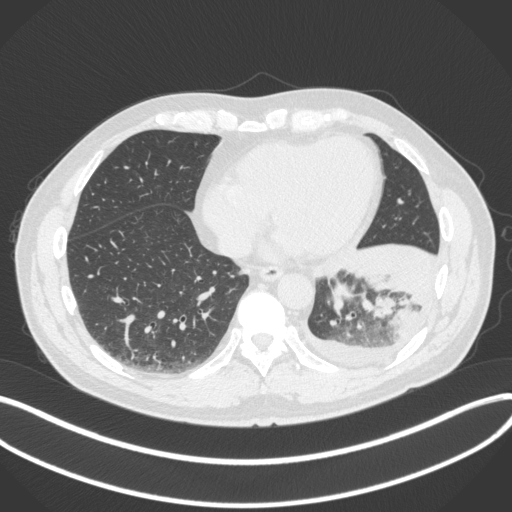
Chest CT, one axial slice. Position 109 of 350 along the scan axis. Reconstruction kernel B31f. Lung window (W 1500 / L -600 HU). 1 mm slice thickness. 512 × 512 image matrix, field of view 400 × 400 mm. Male patient, age 58 years. From the clinical record (not read from this slice): clinical TNM (as recorded): T3 N1 M1b.
Annotated regions visible in this slice (rectangle marked by the reading radiologist):
- lung tumour (recorded histology: small cell carcinoma): bounding box <327,275,355,314> (left, top, right, bottom; pixels)